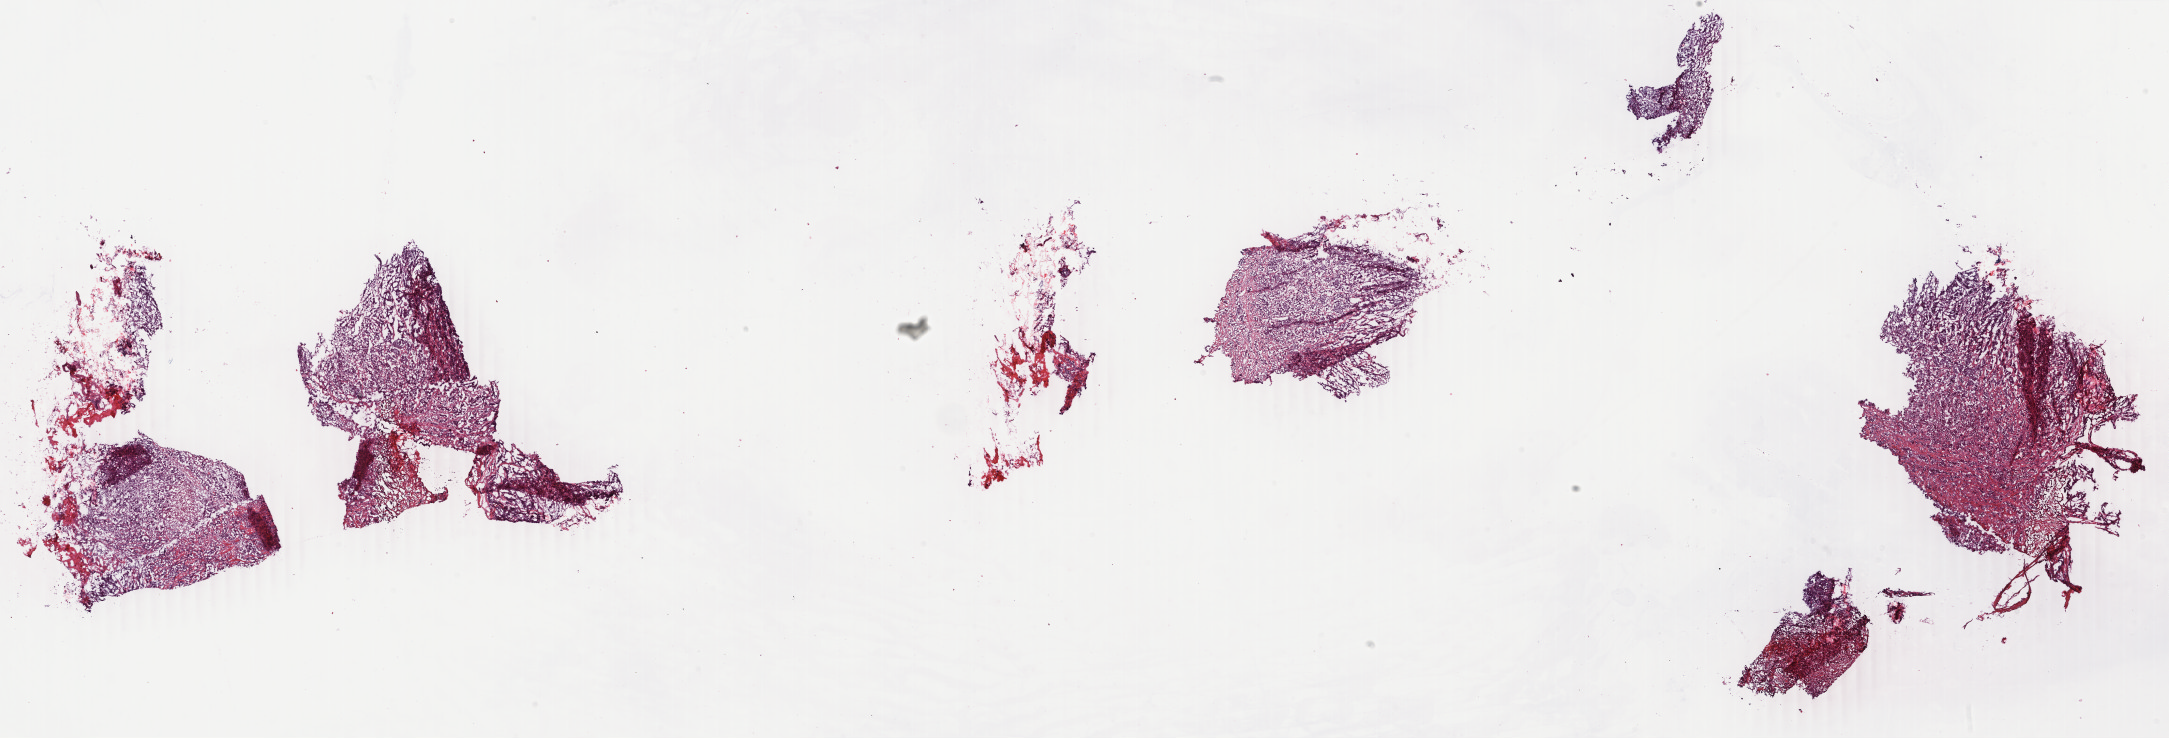
Digitized H&E tissue section (whole slide) — low-resolution overview of the scanned area, about 34.5 x 11.7 mm (slide scanned at 40x). Frozen section. Sample: primary tumour, breast. Patient: female, age at initial diagnosis 39 years. Pathologist review of this section (percent, as recorded): tumour cells 65%, tumour nuclei 65%, normal cells 0%, stromal cells 25%, necrosis 10%. Infiltration values recorded for this section: lymphocyte infiltration 2%, monocyte infiltration 2%, neutrophil infiltration 2%.
- AJCC pathologic stage: IIA
- laterality: right
- lymph nodes positive (case pathology): 0 of 2 examined
- histologic diagnosis: Infiltrating duct carcinoma, NOS